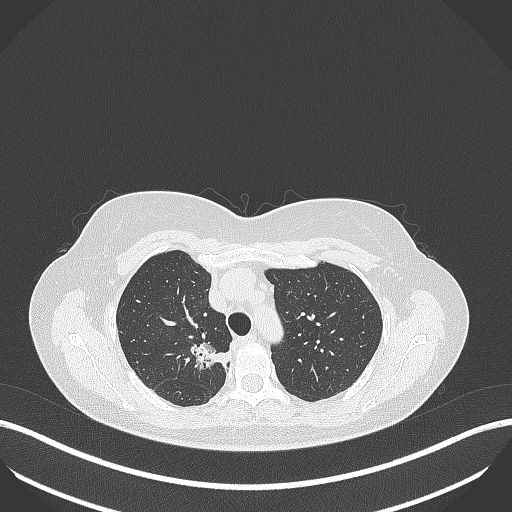
Chest CT, one axial slice. Position 299 of 386 along the scan axis. 120 kVp. Lung window (W 1500 / L -600 HU). 512 × 512 image matrix. Female patient, age 65 years. Case-level facts recorded for this patient, not image findings: clinical TNM (as recorded): T1b N0 M0.
Annotated regions visible in this slice (rectangle marked by the reading radiologist):
- lung tumour (recorded histology: adenocarcinoma): bounding box <186,336,229,374> (left, top, right, bottom; pixels)